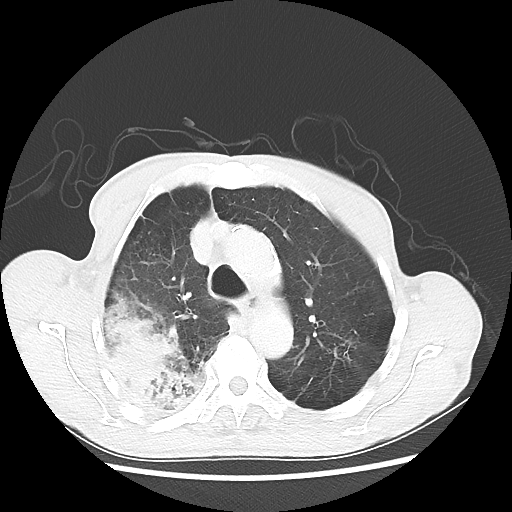
Chest CT, one axial slice. Slice 40 of 58 in the series (ordered by position). Lung window (W 1500 / L -600 HU). 5 mm slice thickness. 512 × 512 image matrix, field of view 351 × 351 mm. Male patient, age 75 years. From the clinical record (not read from this slice): clinical TNM (as recorded): T4 N1 M1.
Structures marked on this image (bounding box drawn by a radiologist):
- lung tumour (recorded histology: adenocarcinoma): bounding box [x1, y1, x2, y2] px = [87, 289, 209, 418]